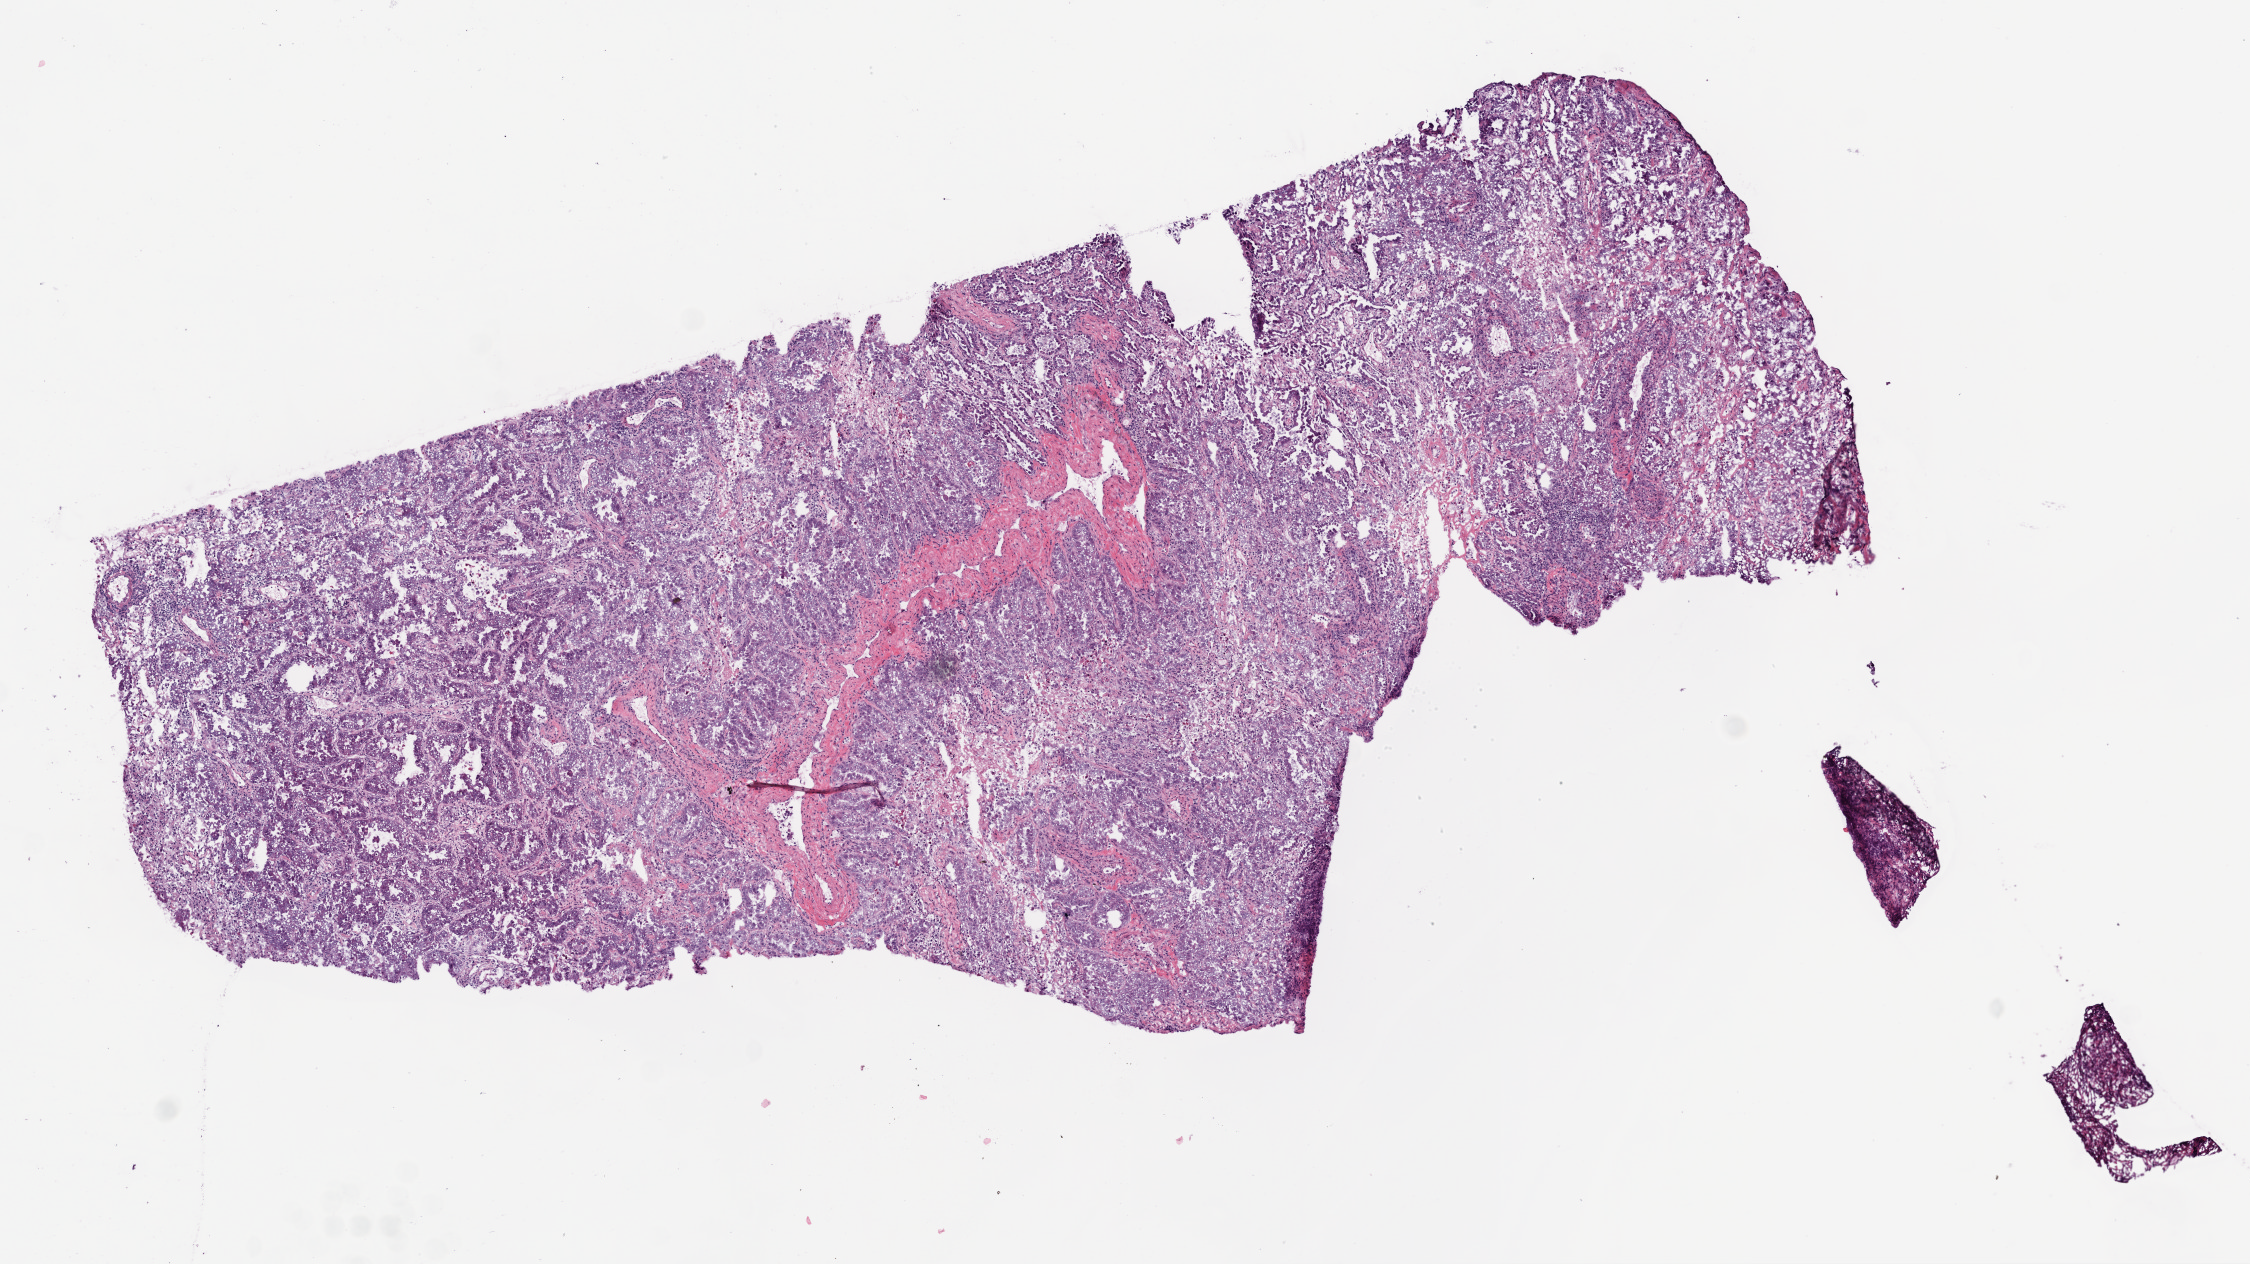
Whole-slide histology image, Hematoxylin and eosin (H&E) stained, low-resolution overview of the scanned area, about 9.0 x 5.1 mm (slide scanned at 20x); frozen section from the bottom of the tissue portion; lung, primary tumour sample. Patient: female, age at initial diagnosis 57 years. Composition of this section per pathologist review: tumour cells 80%, tumour nuclei 70%, normal cells 0%, stromal cells 10%, necrosis 10%.
• laterality: right
• histologic diagnosis: Adenocarcinoma, NOS (lower lobe, lung)
• AJCC pathologic stage: IIB
• TNM: T2 N1 M0